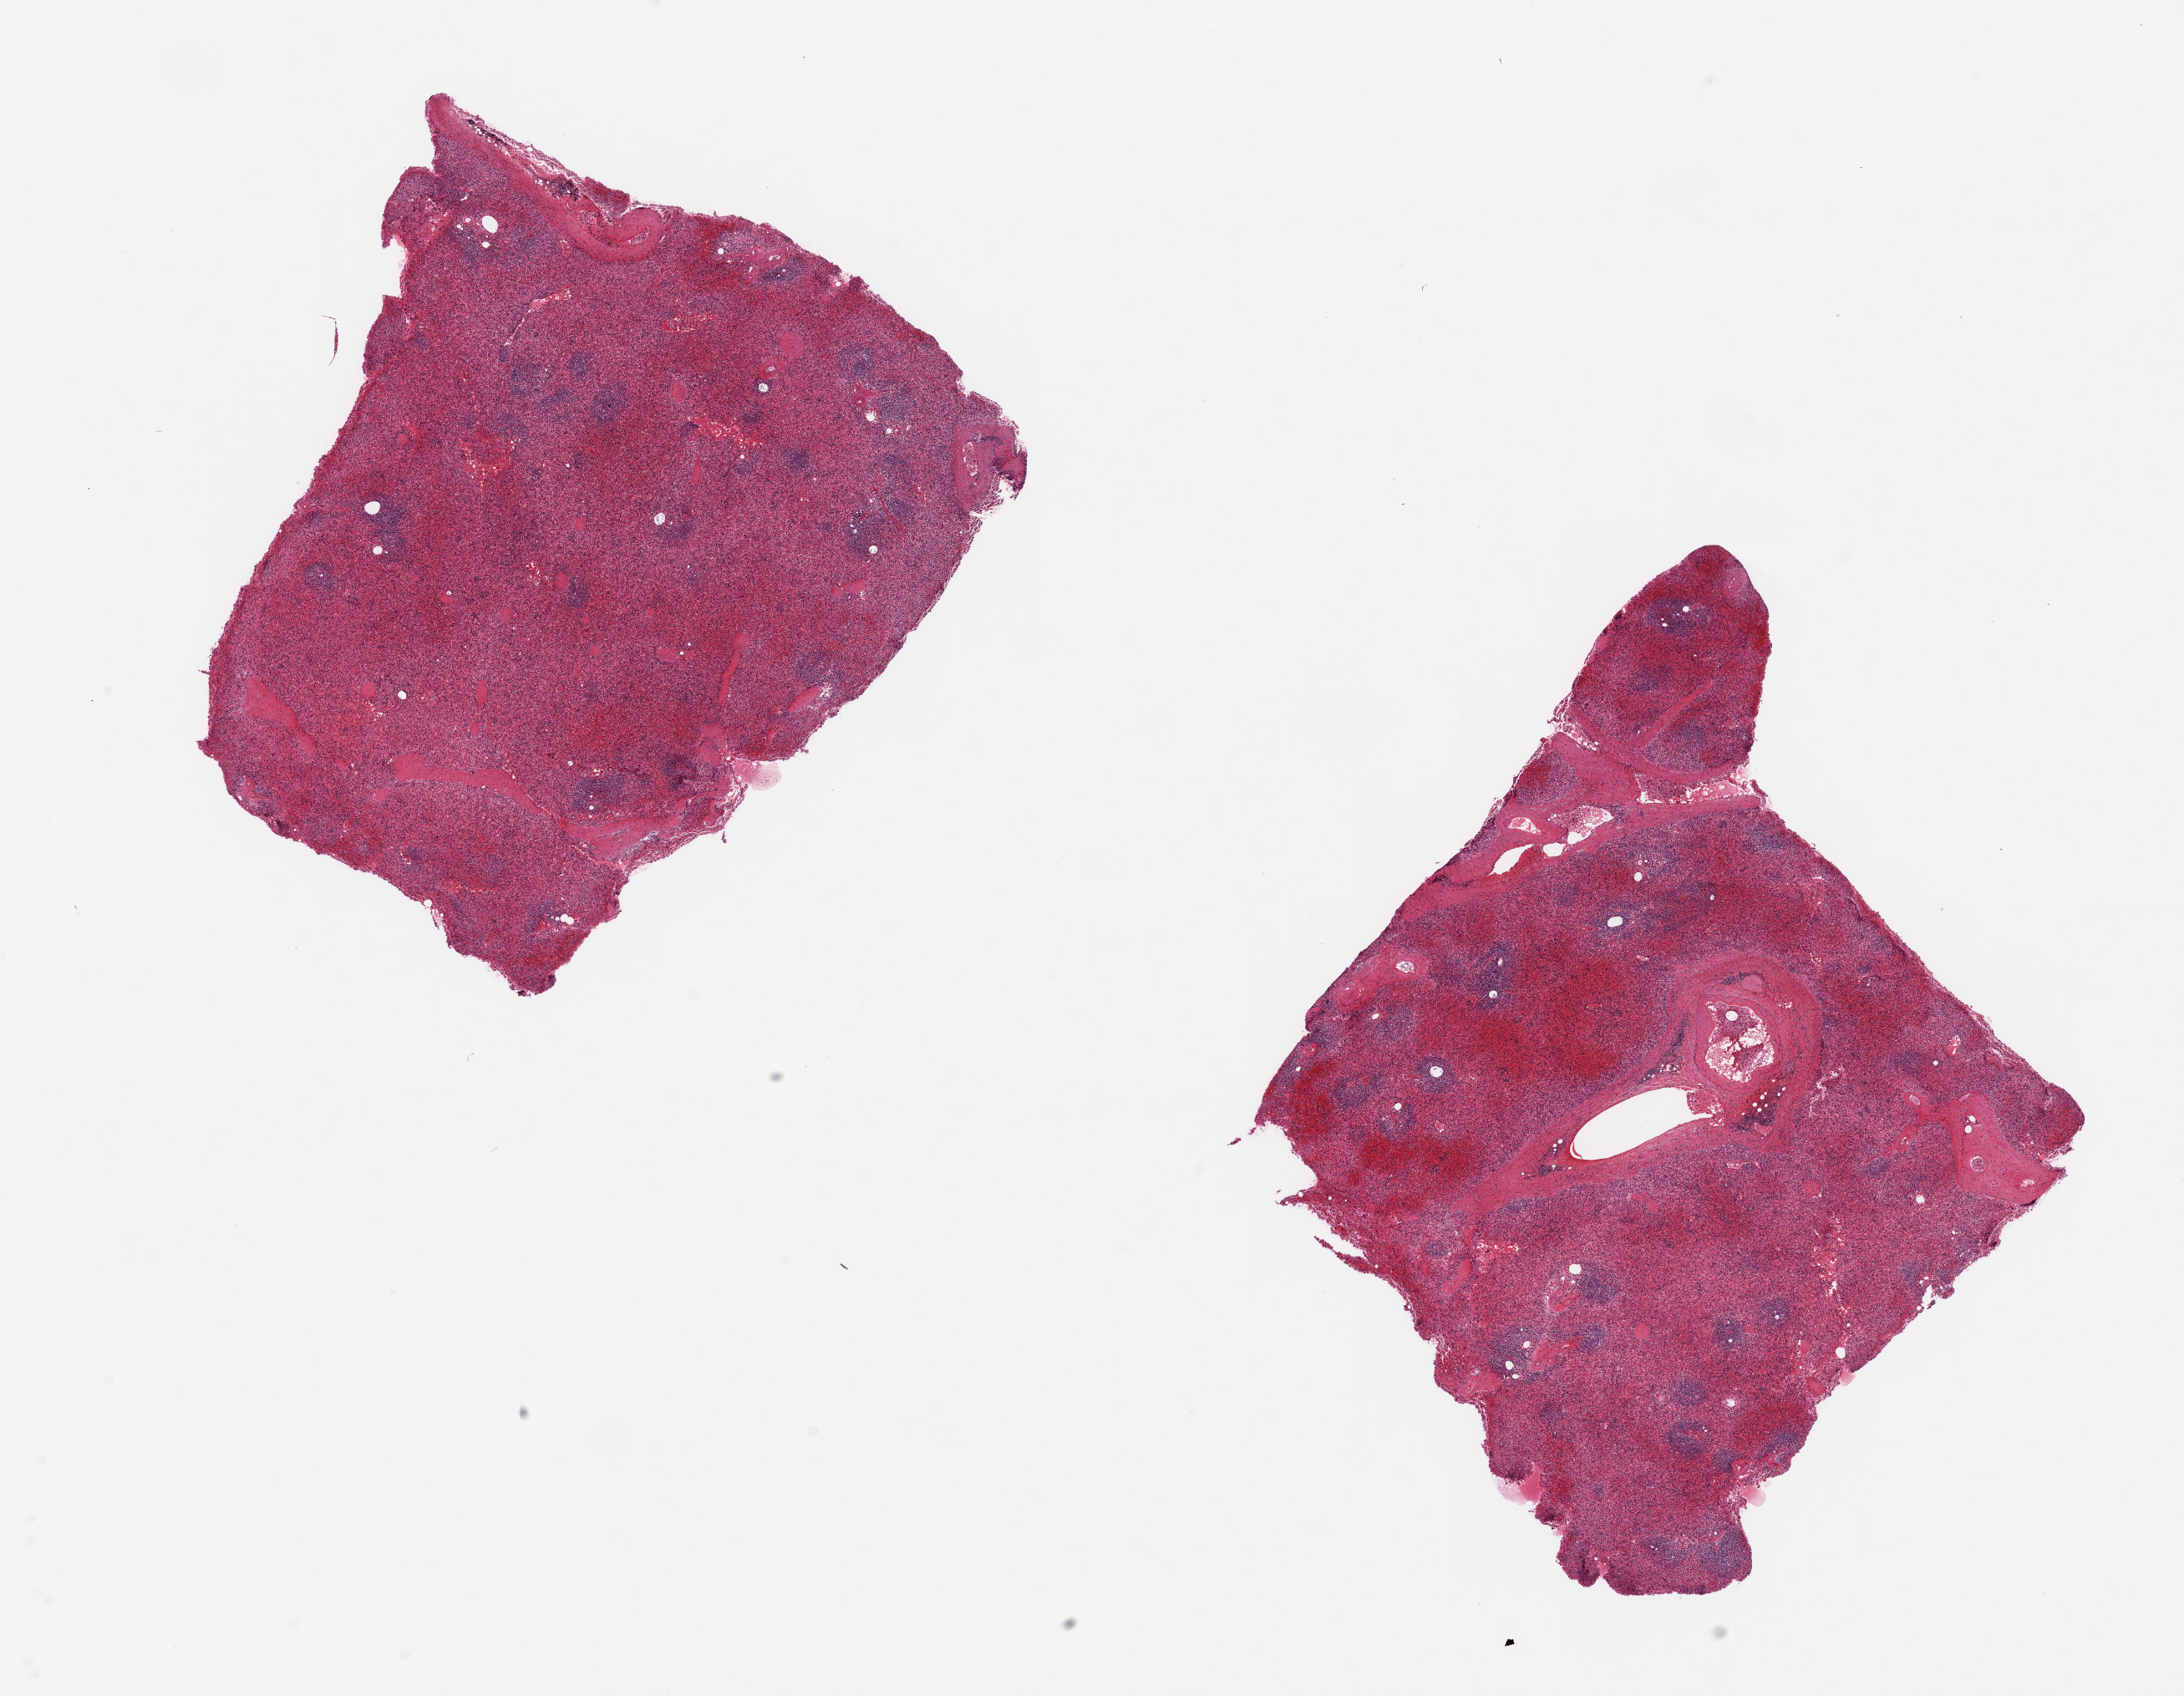
Whole-slide image, haematoxylin and eosin stain, brightfield — shown as a low-resolution overview of the whole scanned area (about 20.7 x 16.1 mm, from a 20x scan). PAXgene-fixed, paraffin-embedded tissue. Sampled site (target tissue): spleen. Donor tissue sample. Donor: male.
- reviewer comment on this tissue sample: 2 pieces, 7x7 & 7x6.5mm; moderately congested